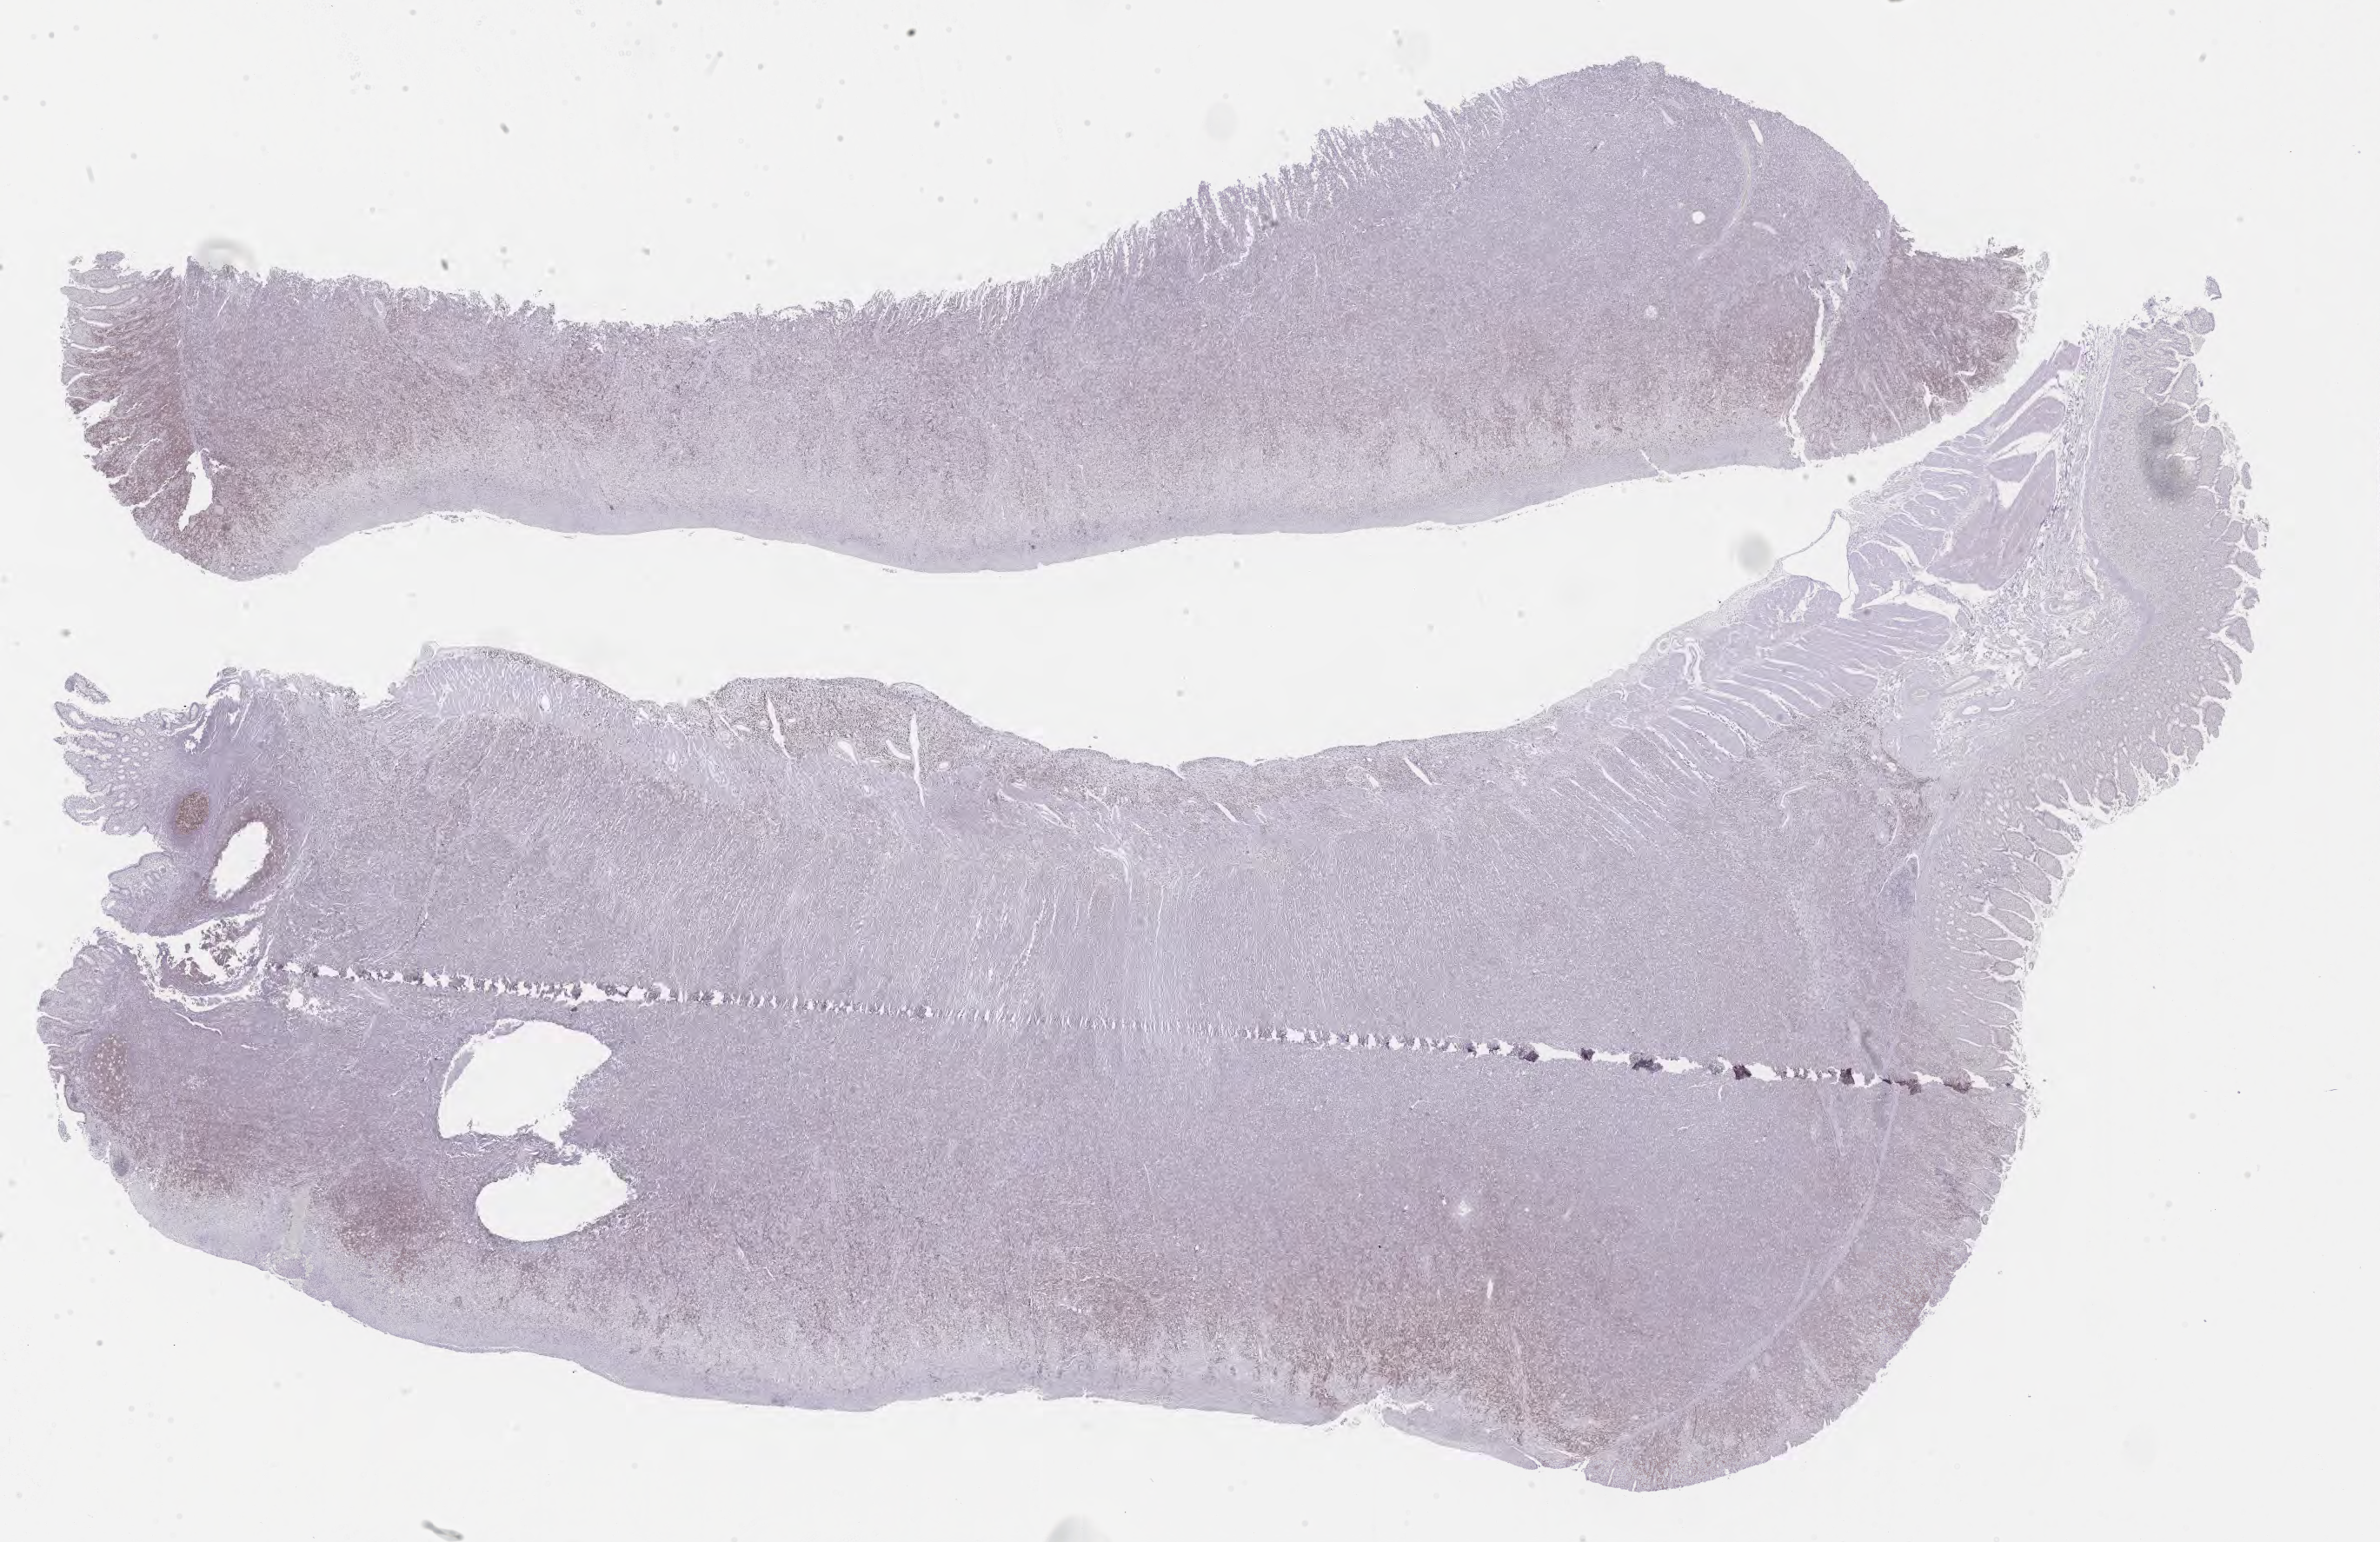
IHC for BCL6, whole-slide image, shown as a low-resolution overview of the whole scanned area (about 22.1 x 14.3 mm); tumor tissue. Female patient, 27 years old.
- diagnosis: Burkitt lymphoma, NOS